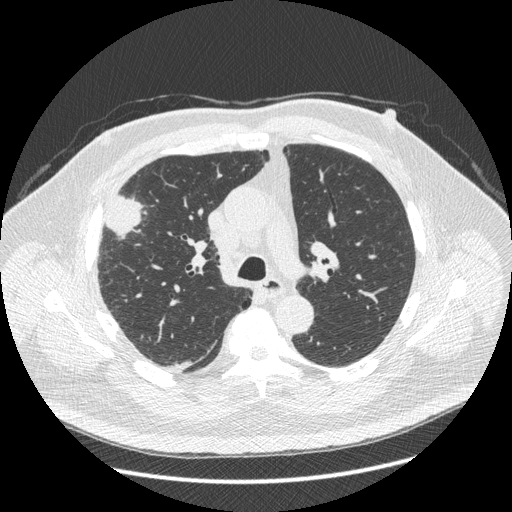
Low-dose screening chest CT, axial slice. Third screening round (two years after baseline). Lung window (W 1500 / L -600 HU). Standard (soft-tissue) reconstruction kernel (STANDARD). 512 × 512 image matrix. Male, age 66 years at enrolment. Current smoker at enrolment.
Expert reader's lesion annotation, bounding box [x1, y1, x2, y2] px = [86, 186, 145, 265]. Reader record for this screening exam (exam-level; its link to the box is not recorded): non-calcified nodule or mass ≥4 mm, right upper lobe, 48 × 25 mm, spiculated (stellate) margins, soft tissue attenuation, pre-existing on the prior screen: no. Official screen result: positive, other. Later outcome: lung cancer diagnosed 35 days after this screen — non-small cell carcinoma, right upper lobe, stage IV (AJCC 6th edition), 50 mm at pathology.